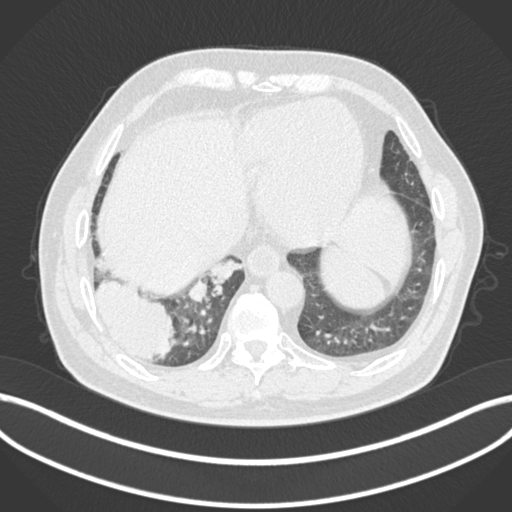
Chest CT, one axial slice. Reconstruction kernel B30f. 120 kVp. Lung window (W 1500 / L -600 HU). 1 mm slice thickness. 512 × 512 image matrix, field of view 400 × 400 mm. Patient: male, 59 years.
Structures marked on this image (rectangle marked by the reading radiologist):
- lung tumour (recorded histology: adenocarcinoma): bounding box [x1, y1, x2, y2] px = [90, 274, 175, 365]